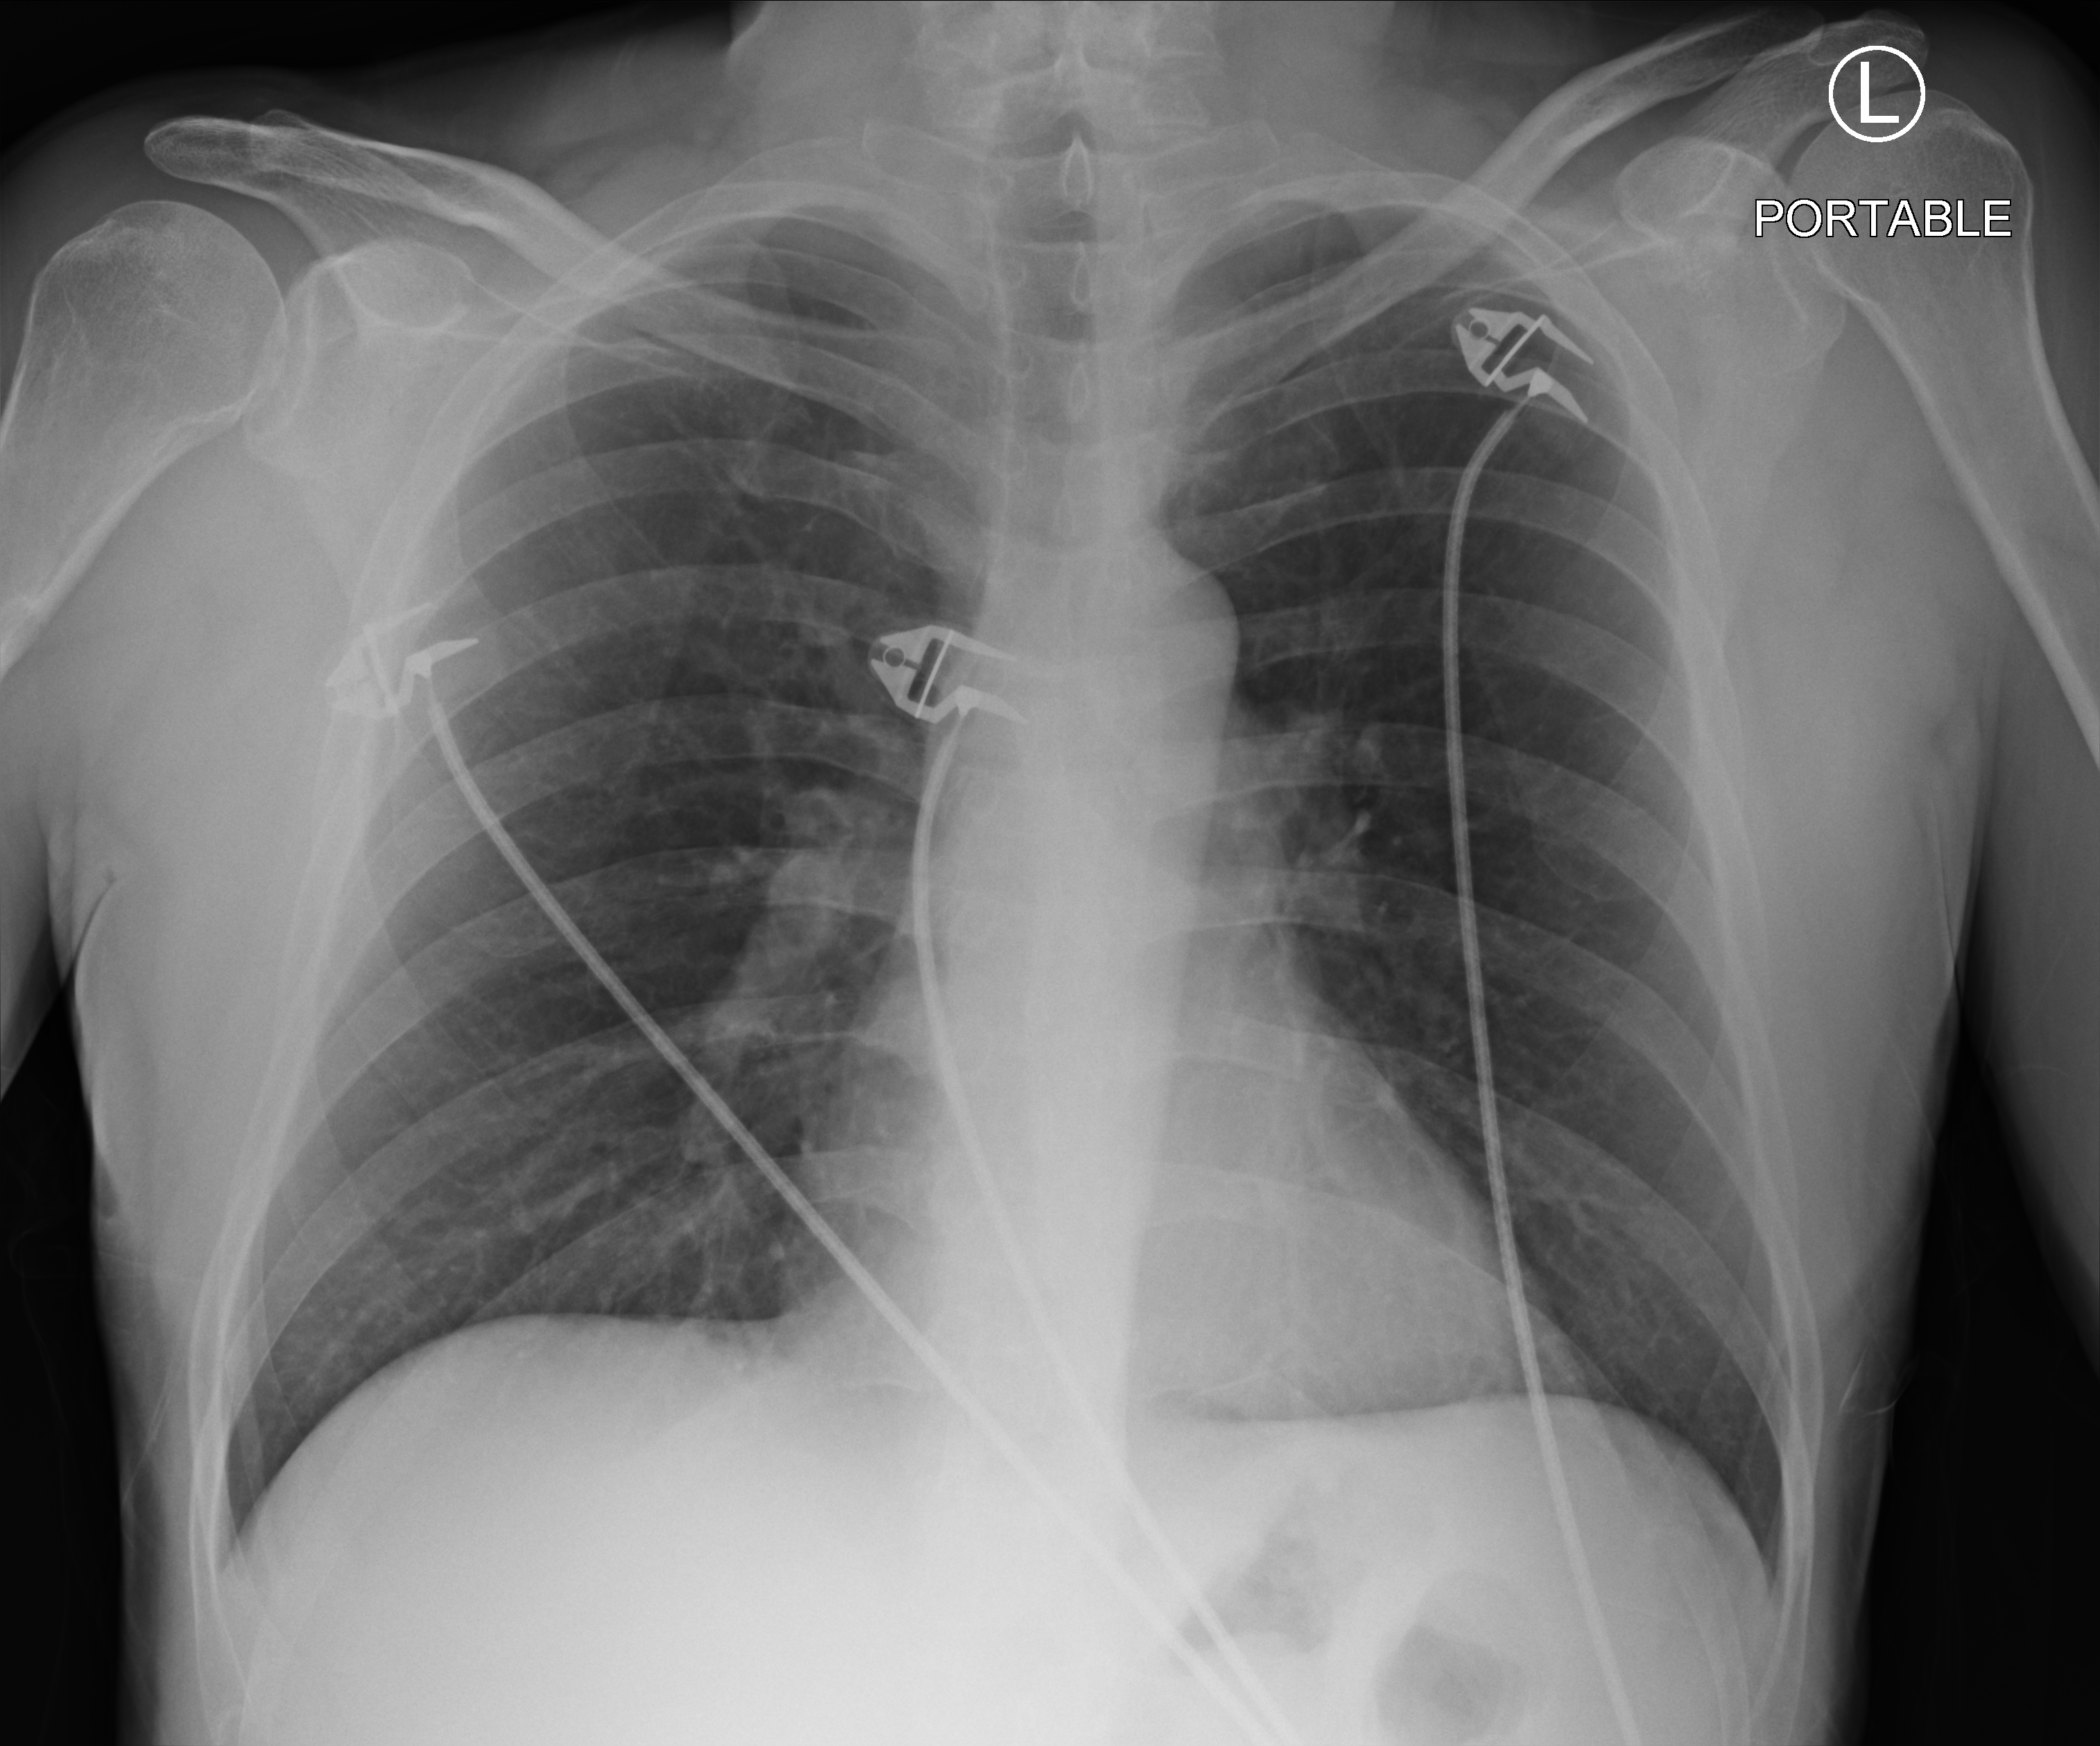
Portable chest radiograph; anteroposterior (AP) projection. Male patient hospitalised with COVID-19, age 18–59 years.
Hospital-stay facts (about this admission, not read from this image; timing relative to this image not recorded): other chronic lung disease (admission record): no; mechanically ventilated during this hospital stay: no; admitted to intensive care during this hospital stay: no.